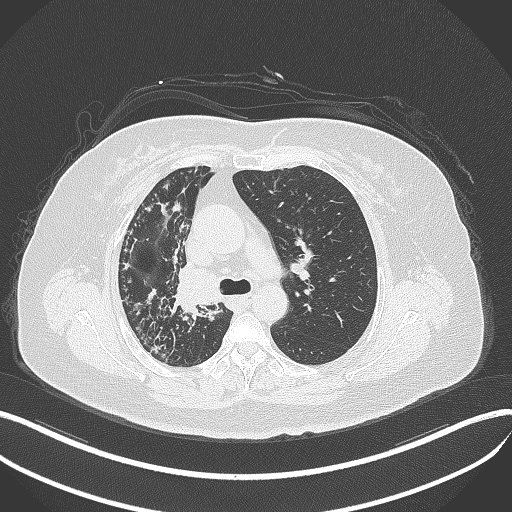
Chest CT, one axial slice. Slice 239 of 376 in the series (ordered by position). Reconstruction kernel B70f. 120 kVp. Lung window (W 1500 / L -600 HU). 1 mm slice thickness. 512 × 512 image matrix, field of view 400 × 400 mm. Patient: female, 60 years. Case-level facts recorded for this patient, not image findings: clinical TNM (as recorded): T1c N0 M0; histopathological grade: G1-G2.
Outlined on this slice (bounding box drawn by a radiologist):
- lung tumour (recorded histology: squamous cell carcinoma): bounding box <169,264,226,311> (left, top, right, bottom; pixels)